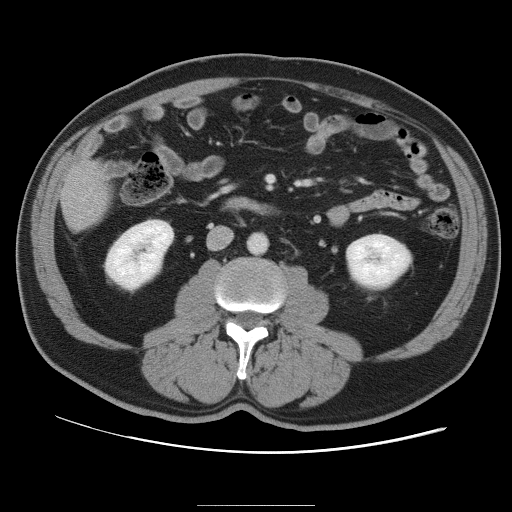
Contrast-enhanced abdominal CT, one axial slice; slice 24 of 105 in the series (ordered by position); 120 kVp; intravenous contrast given; soft-tissue window (W 400 / L 40 HU); 5 mm slice thickness; 512 × 512 image matrix, field of view 399 × 399 mm. Male patient, age 64 years. Case-level facts recorded for this patient, not image findings: diagnosis: colorectal cancer liver metastases, imaged before liver resection; multiple liver metastases: yes; largest metastasis: 3 cm; chemotherapy before resection: yes.
Outlined on this slice (outlined manually by an expert reader):
- liver: box from (x=62, y=164) to (x=109, y=230) px
- planned liver remnant (the part of the liver to remain after resection): (x=62, y=165)–(x=110, y=225)